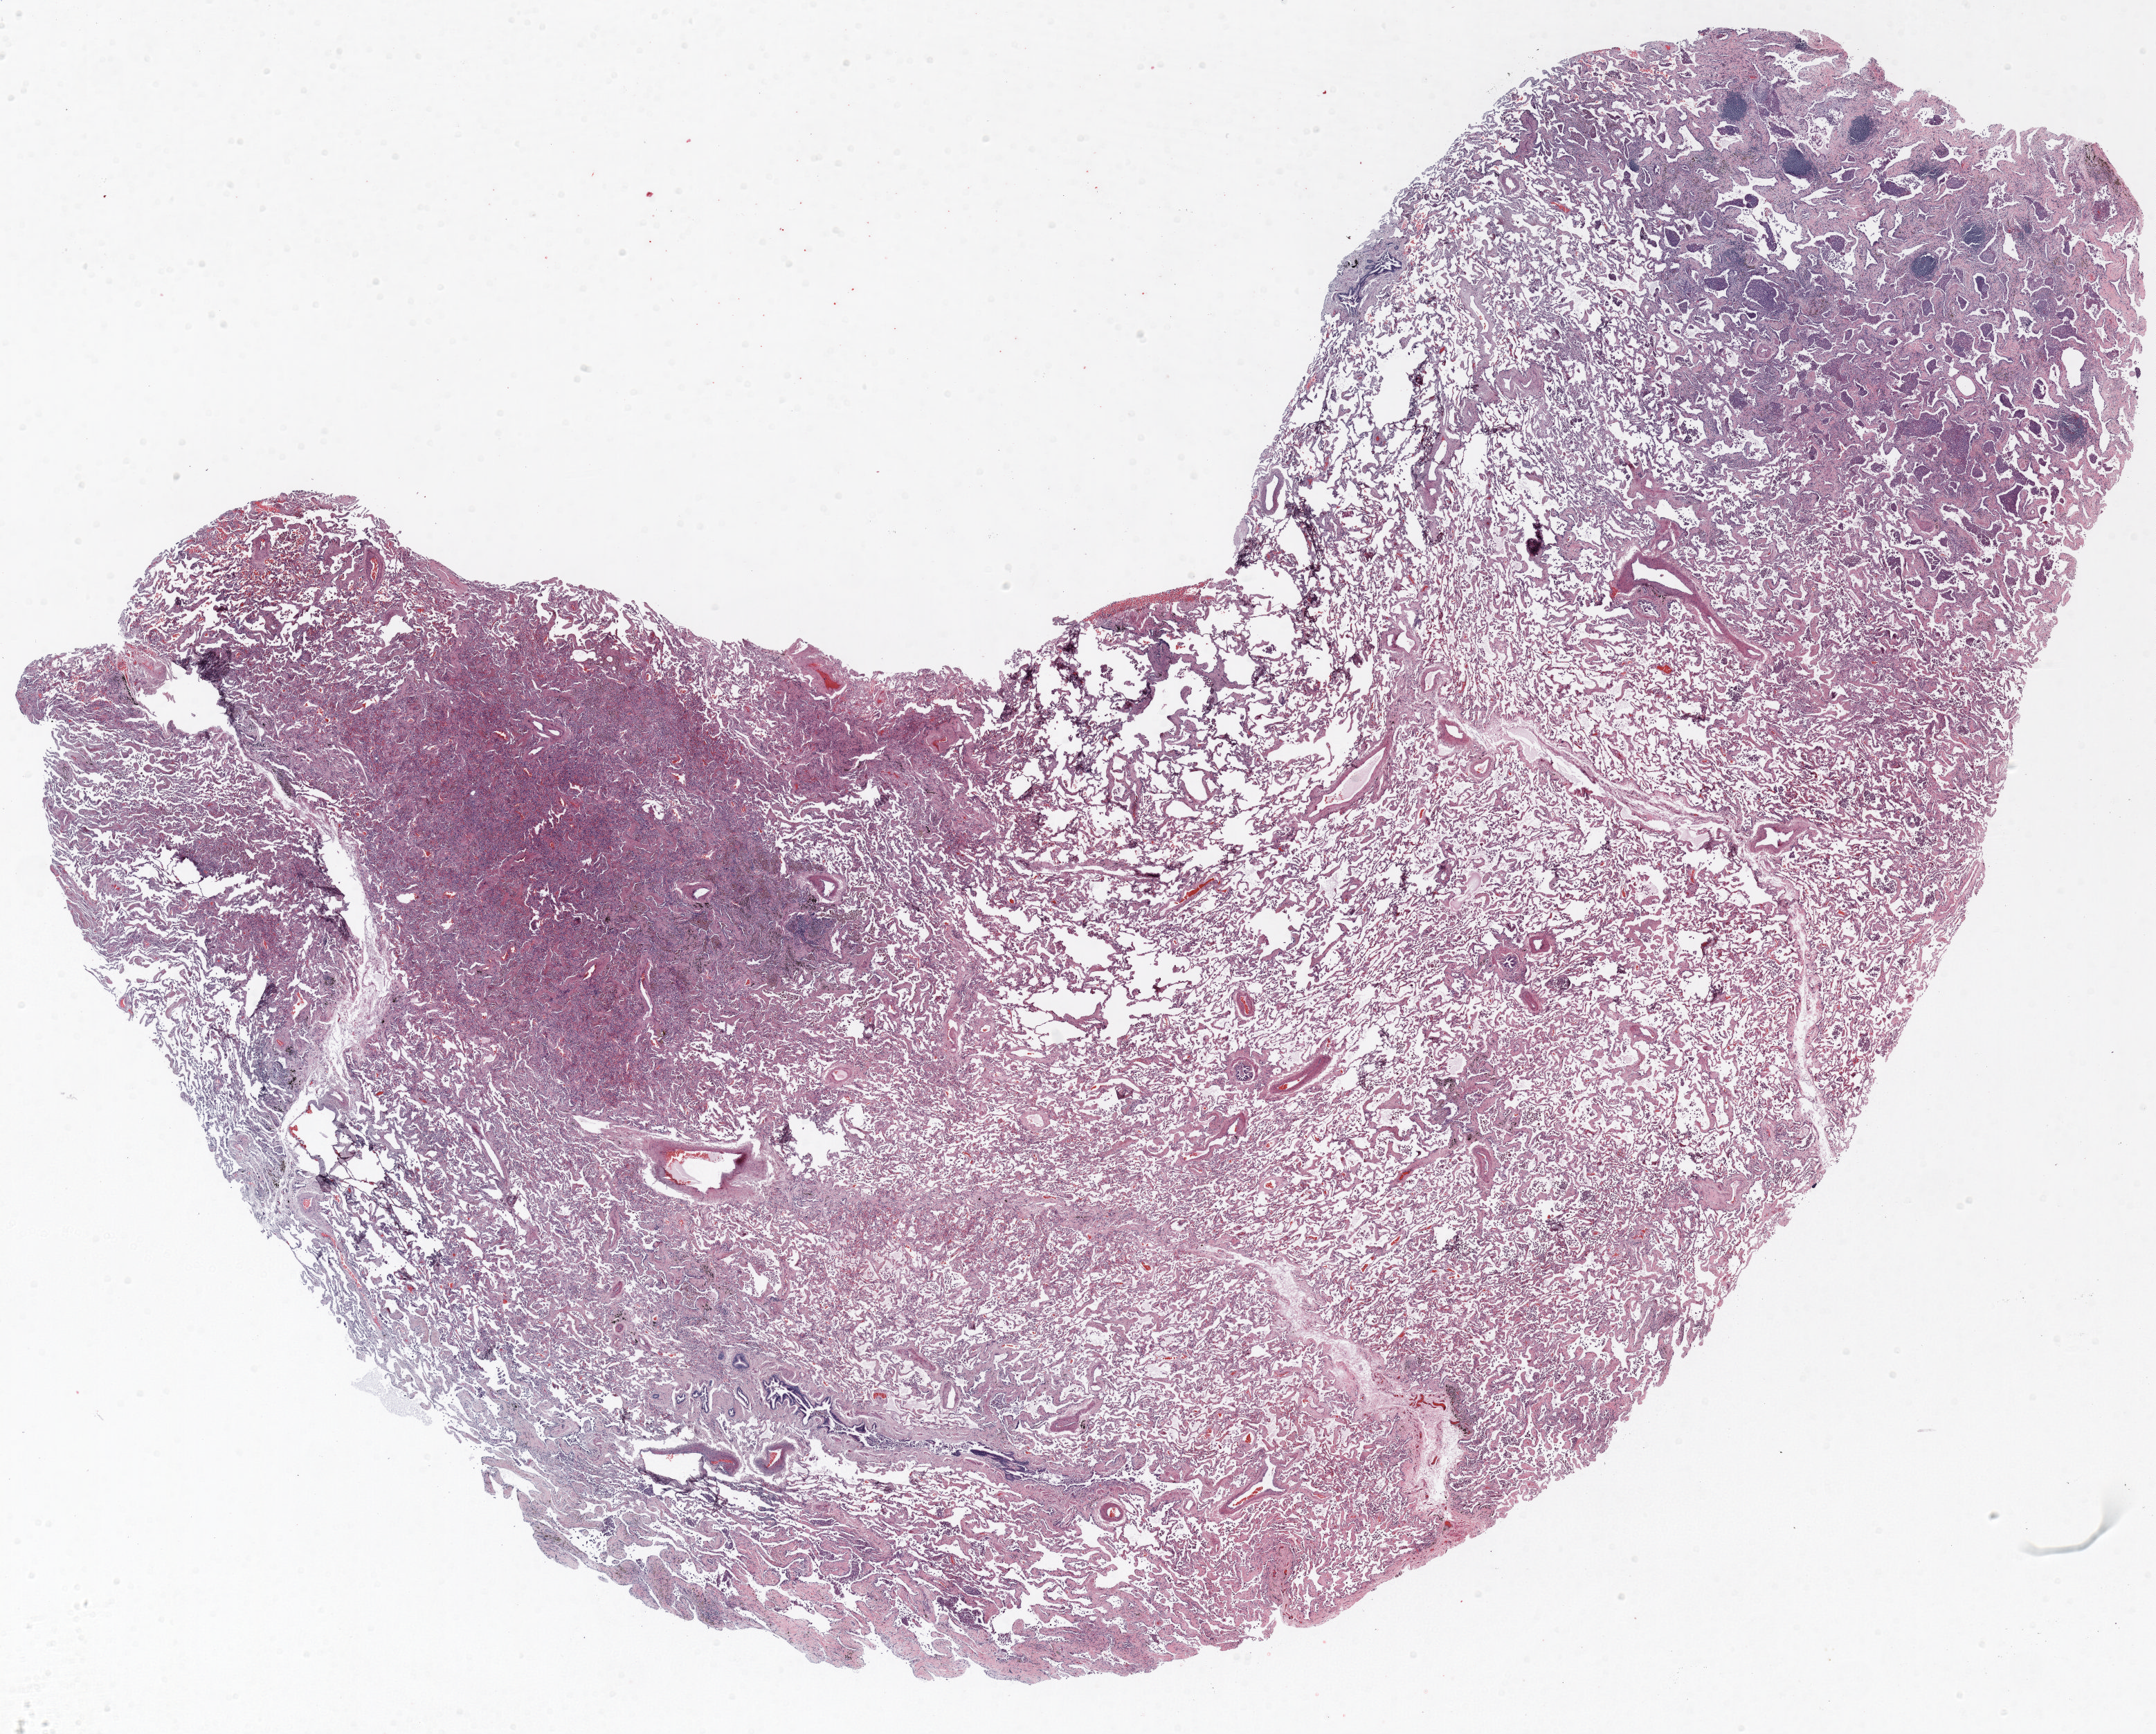
Whole-slide histology image, H&E, shown as a low-resolution overview of the whole scanned area (about 25.0 x 20.1 mm, acquisition: 20x scan). Formalin-fixed paraffin-embedded (FFPE) section. Lung. Male patient, aged 64 at enrolment. Current smoker at enrolment. Grade: poorly differentiated (G3).
Participant's lung-cancer diagnosis: Adenocarcinoma, NOS. ICD-O-3 topography: upper lobe of lung (C34.1). Primary tumour location (clinical record): right upper lobe. Tumour size (pathology): 13 mm. Stage (AJCC 6th edition): IA.